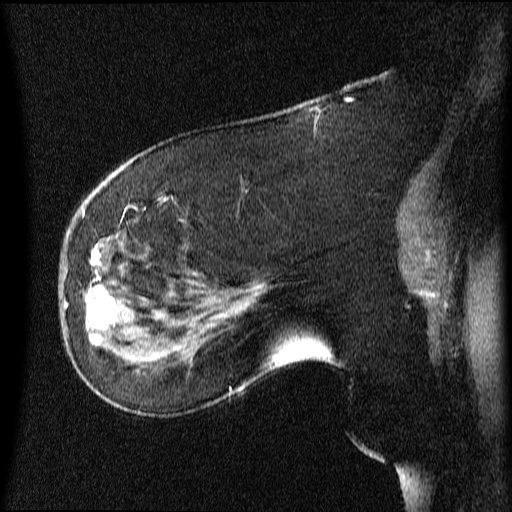
Breast MRI (dynamic contrast-enhanced), one sagittal slice; slice 25 of 64 in the series (ordered by position); dynamic contrast-enhanced series, image 2 of 4 at this slice position (ordered by acquisition); 1.5 T; TE 4.2 ms, TR 9 ms; 512 × 512 image matrix, field of view 200 × 200 mm. Female patient, age 63 years.
Outlined on this slice (semi-automatic segmentation, software-assisted and operator-edited):
- analysis volume of interest (the breast-tissue region the enhancement analysis was run in; not a lesion): box from (x=66, y=272) to (x=131, y=353) px
- tumour enhancement mask (voxels above the 70 % enhancement threshold inside the analysis volume of interest): (x=88, y=276)–(x=118, y=353)